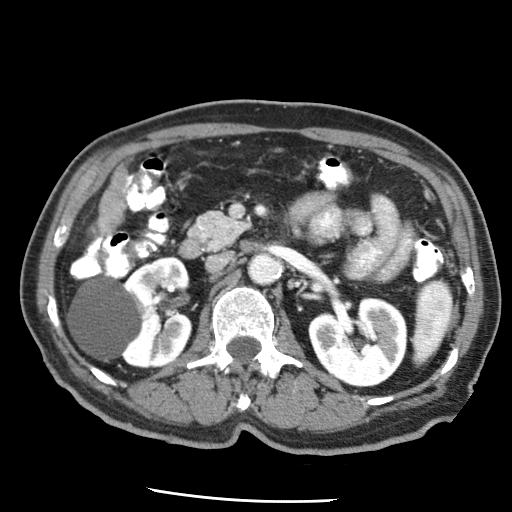
Contrast-enhanced abdominal CT (liver protocol), one axial slice; slice 9 of 79 in the series (ordered by position); reconstruction kernel STANDARD; soft-tissue window (W 400 / L 40 HU); 2.5 mm slice thickness; 512 × 512 image matrix. Case-level facts recorded for this patient, not image findings: diagnosis: hepatocellular carcinoma (patient treated with transarterial chemoembolisation; whether this scan precedes or follows treatment is not stated here); TNM stage (as recorded): Stage-IIIA.
Structures marked on this image (semi-automatic segmentation, software-assisted and operator-edited):
- liver parenchyma outside the tumour (the mass and vessels are separate outlines, so this box may not span the whole liver): bounding box [x1, y1, x2, y2] px = [100, 174, 127, 232]